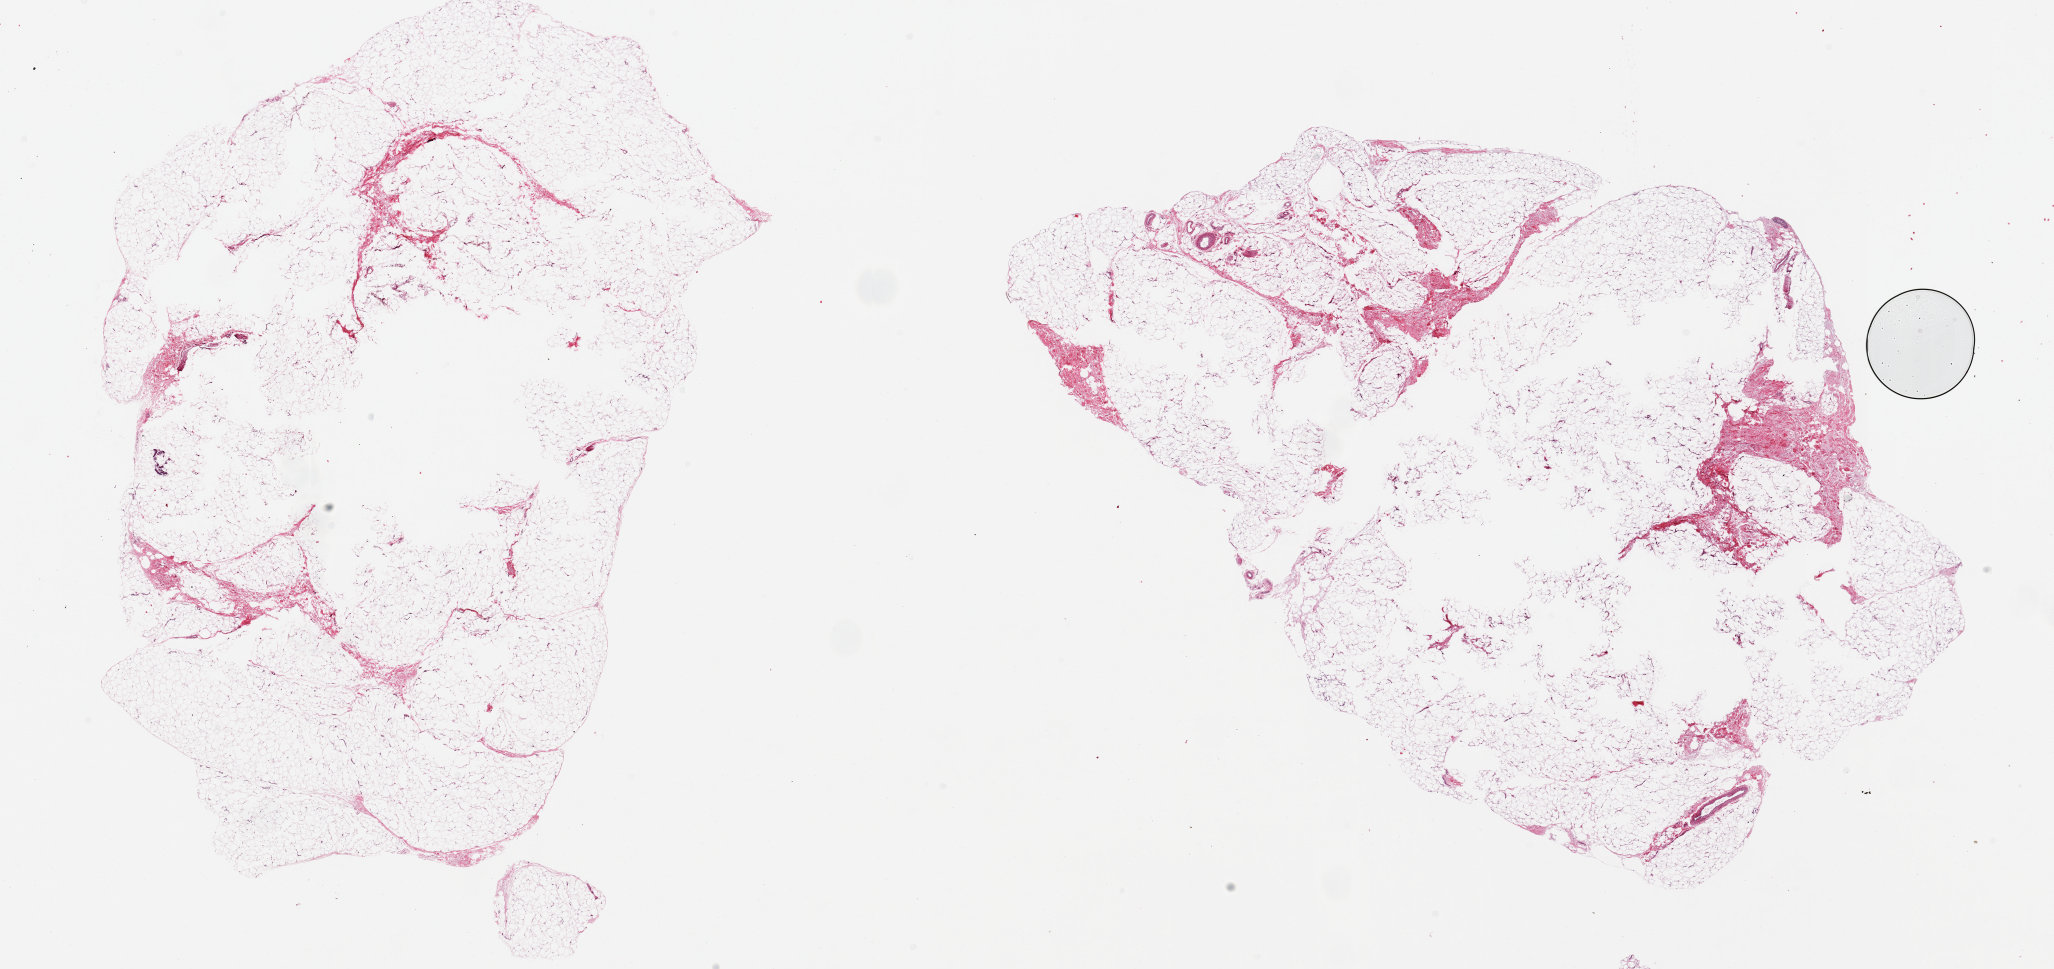
Digitized H&E-stained section, low-resolution overview of the scanned area, about 32.5 x 15.3 mm; PAXgene-fixed, paraffin-embedded tissue; target tissue: adipose tissue; tissue donor sample. Donor sex: male.
Pathologist's review note for this sample: 2 pieces, 15x10 & 16x11mm.